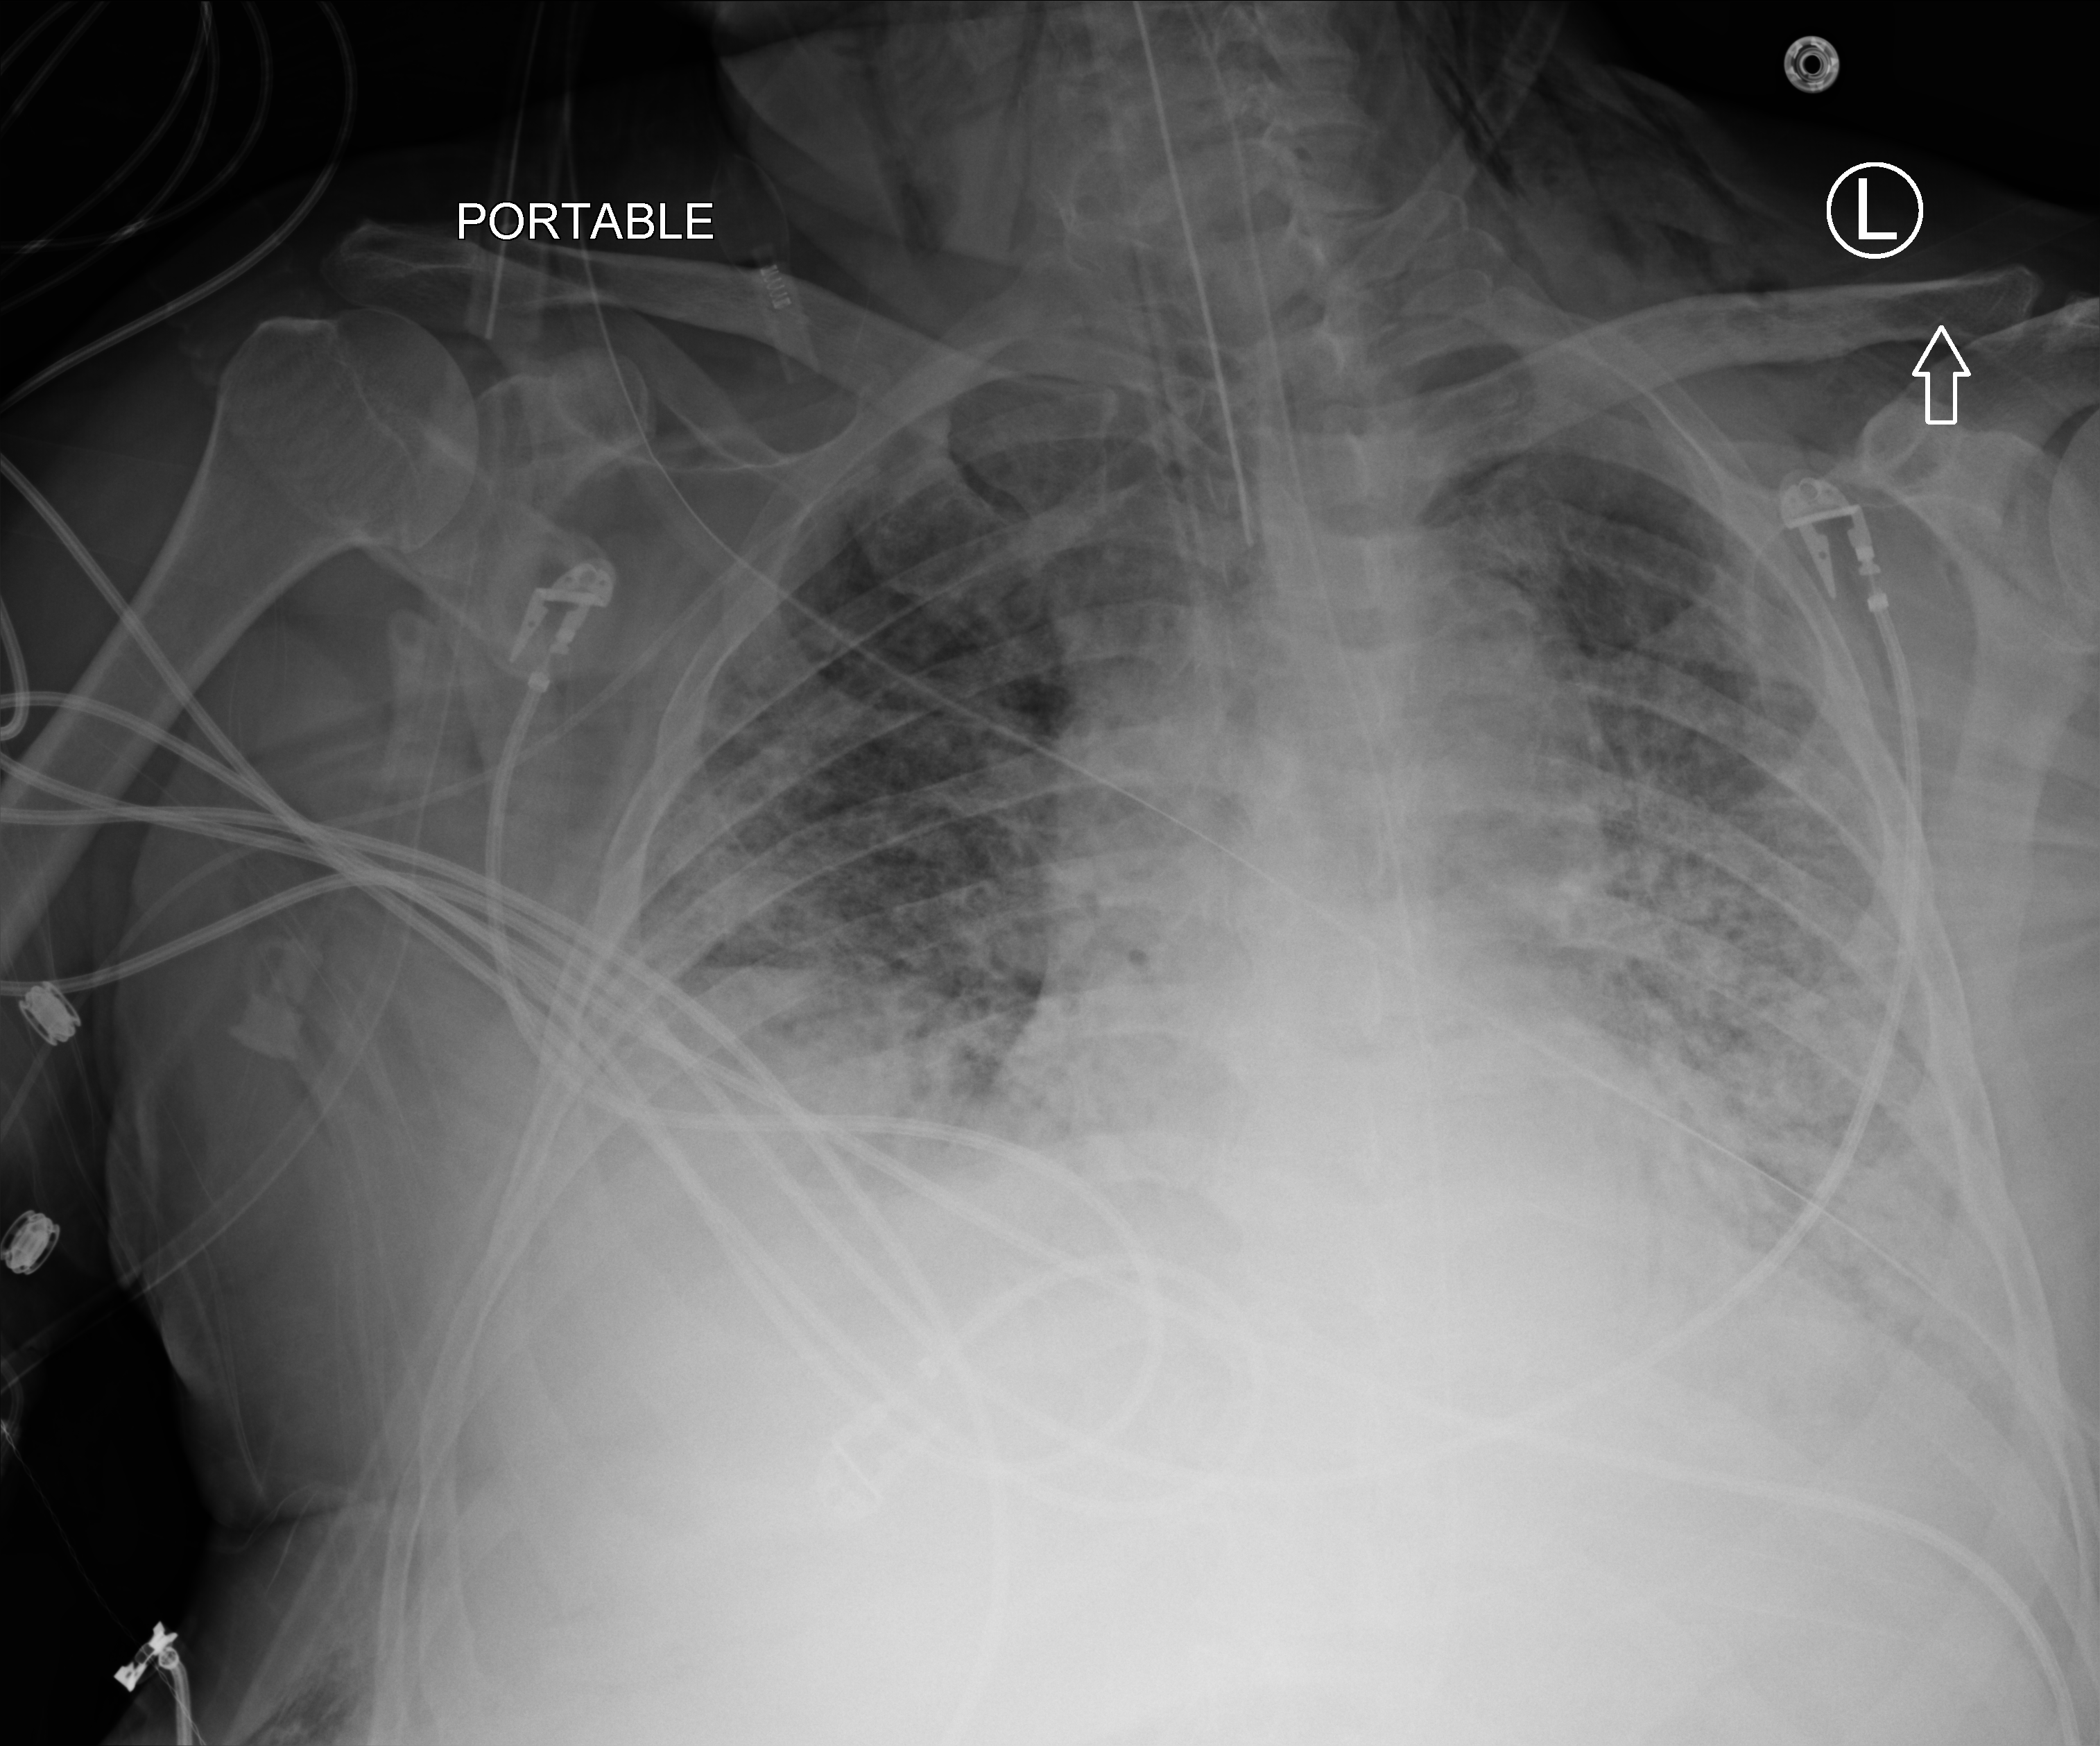
Bedside chest radiograph (computed radiography), anteroposterior (AP) projection. Male patient hospitalised with COVID-19, age 60–74 years.
Hospital-stay facts (about this admission, not read from this image; timing relative to this image not recorded): smoking status (admission record): former; admitted to intensive care during this hospital stay: yes.